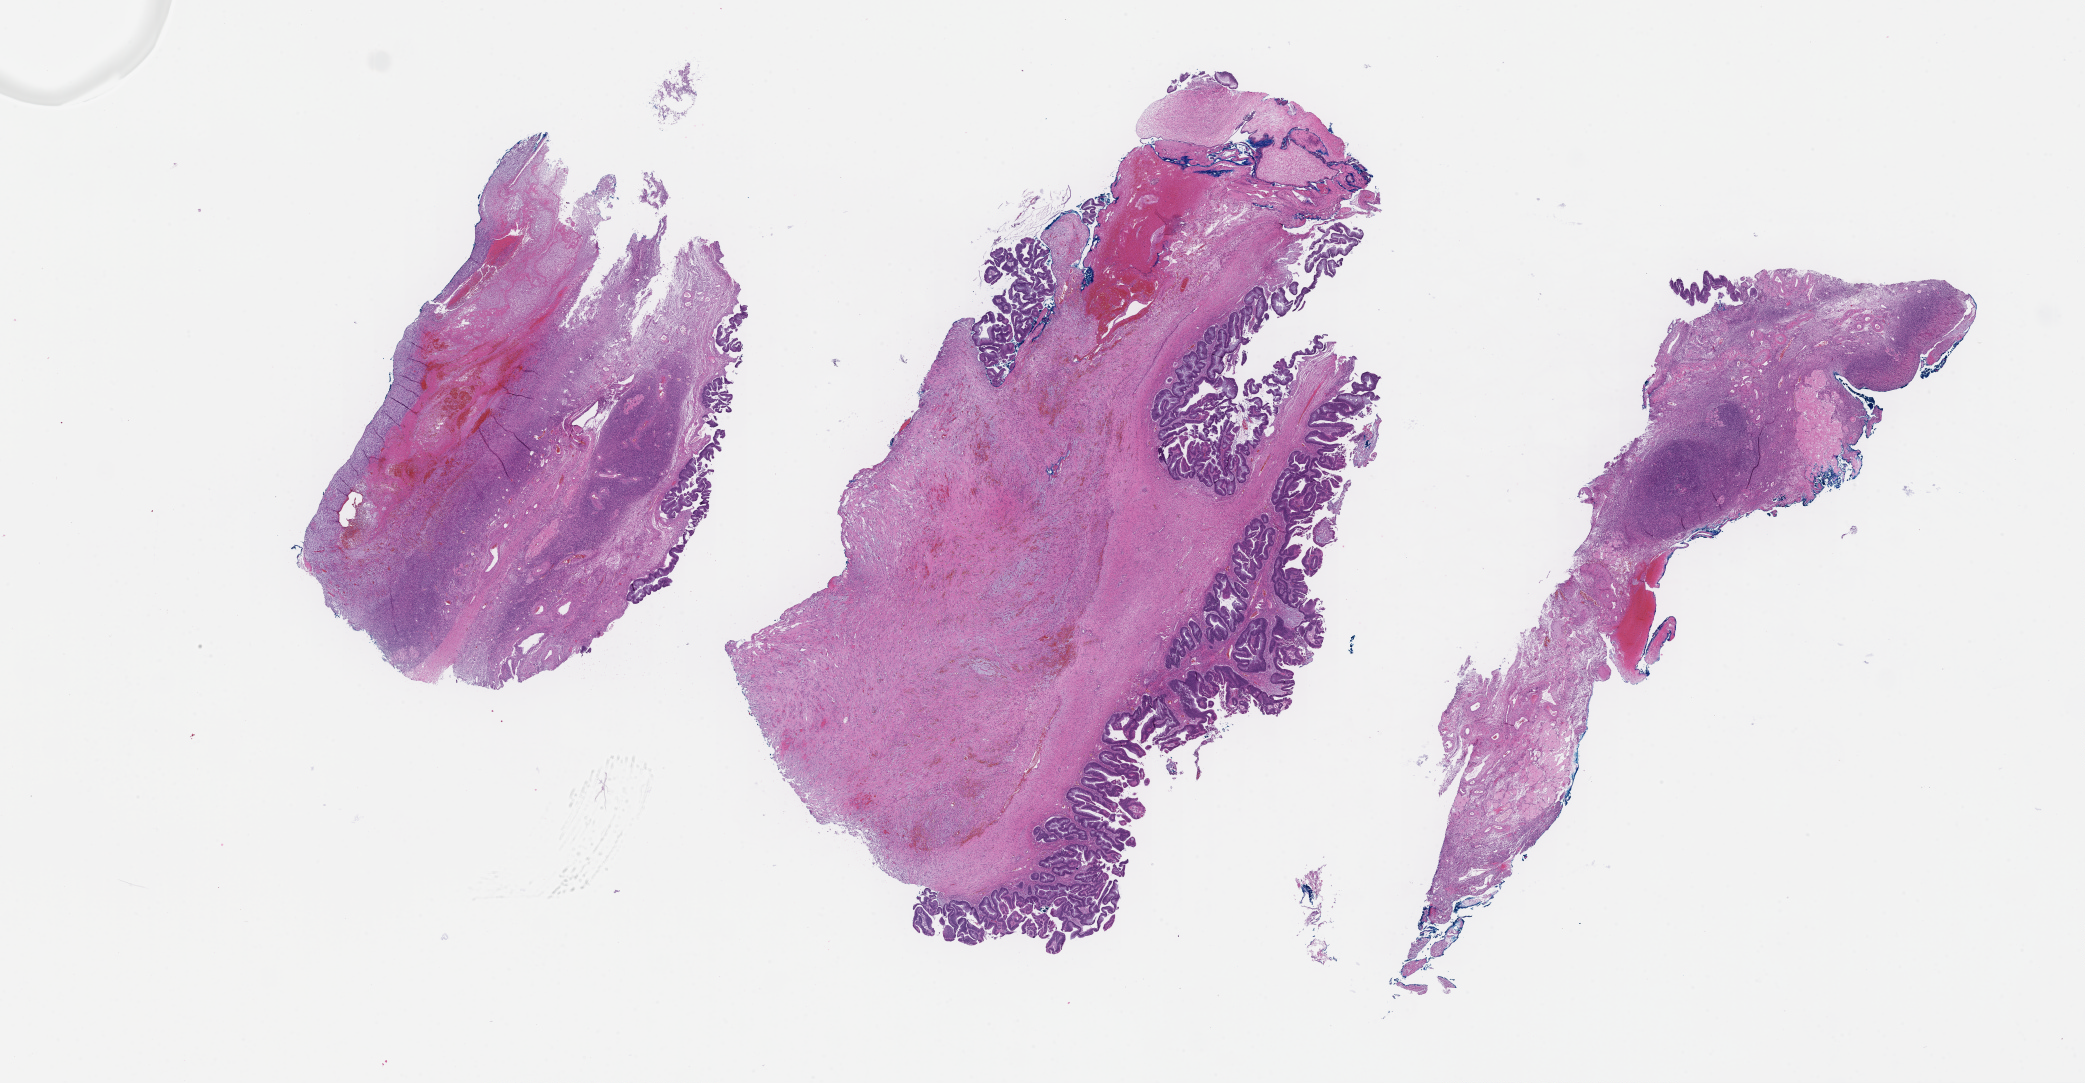
Digitized hematoxylin and eosin (H&E)-stained section — shown as a low-resolution overview of the whole scanned area (about 33.7 x 17.5 mm), formalin-fixed paraffin-embedded section, specimen time point: archival tissue. Patient sex: female.
This section: metastasis (sampled organ not recorded). Patient diagnosis (primary): Colorectal Carcinoma.